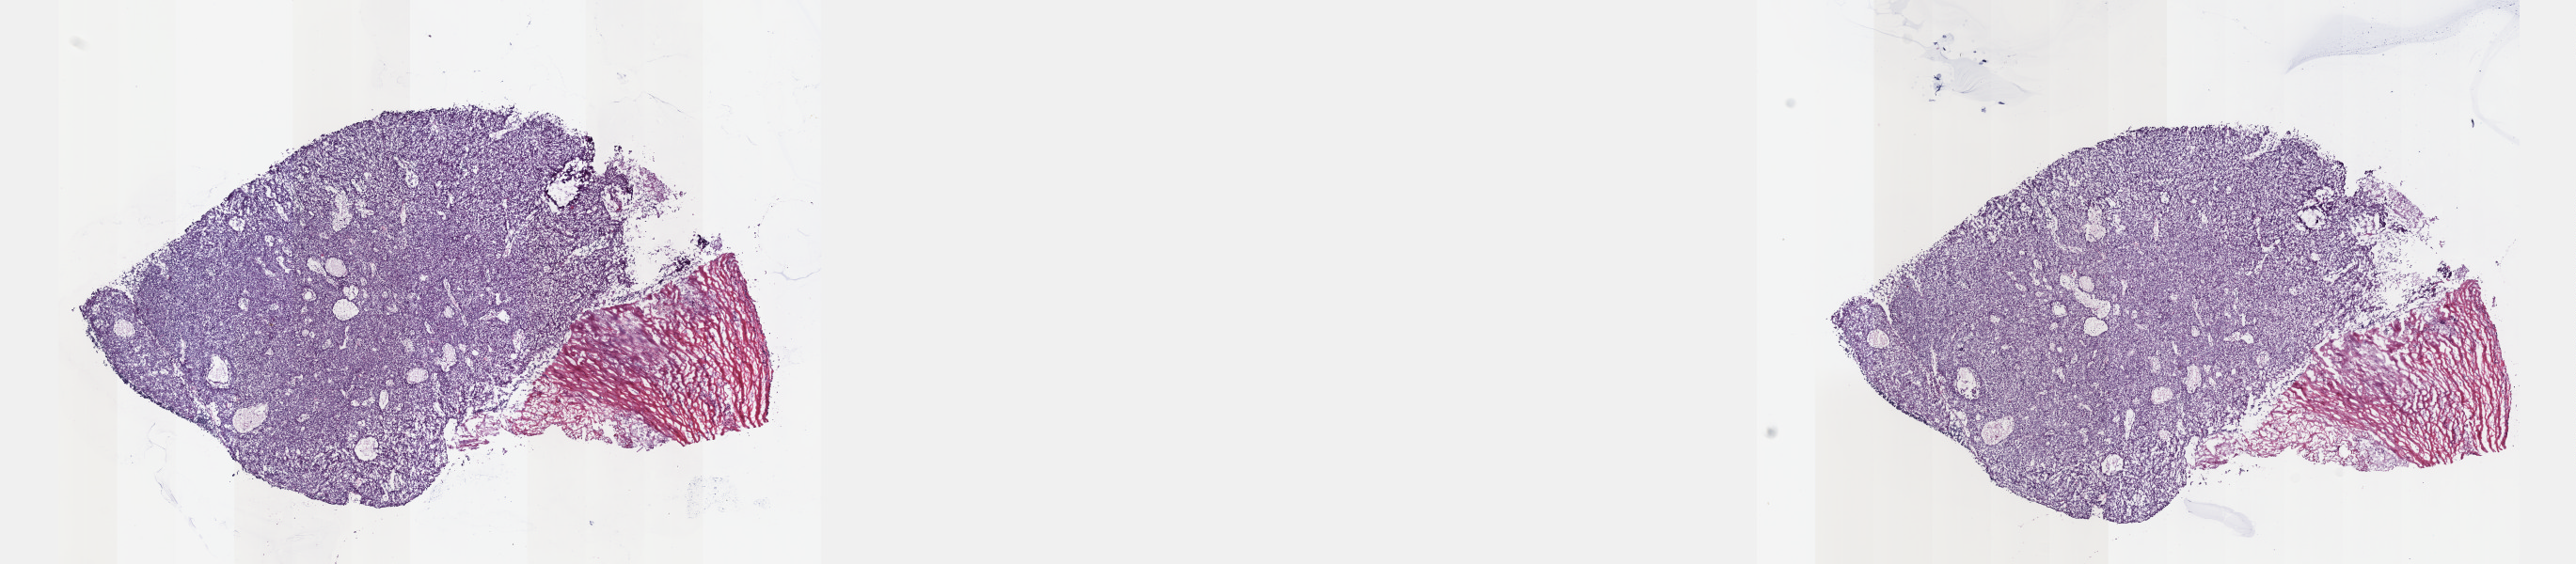
Digitized H&E tissue section (whole slide), low-resolution overview of the scanned area, about 22.1 x 4.8 mm; frozen section from the top of the tissue portion; sample: primary tumour, thymus. Patient: male, age at initial diagnosis 51 years. Pathologist review of this section (percent, as recorded): tumour cells 80%, tumour nuclei 70%, normal cells 20%, stromal cells 0%, necrosis 0%. Infiltration values recorded for this section: lymphocyte infiltration 3%, monocyte infiltration 0%, neutrophil infiltration 0%.
Histologic diagnosis: Thymoma, type B2, malignant.